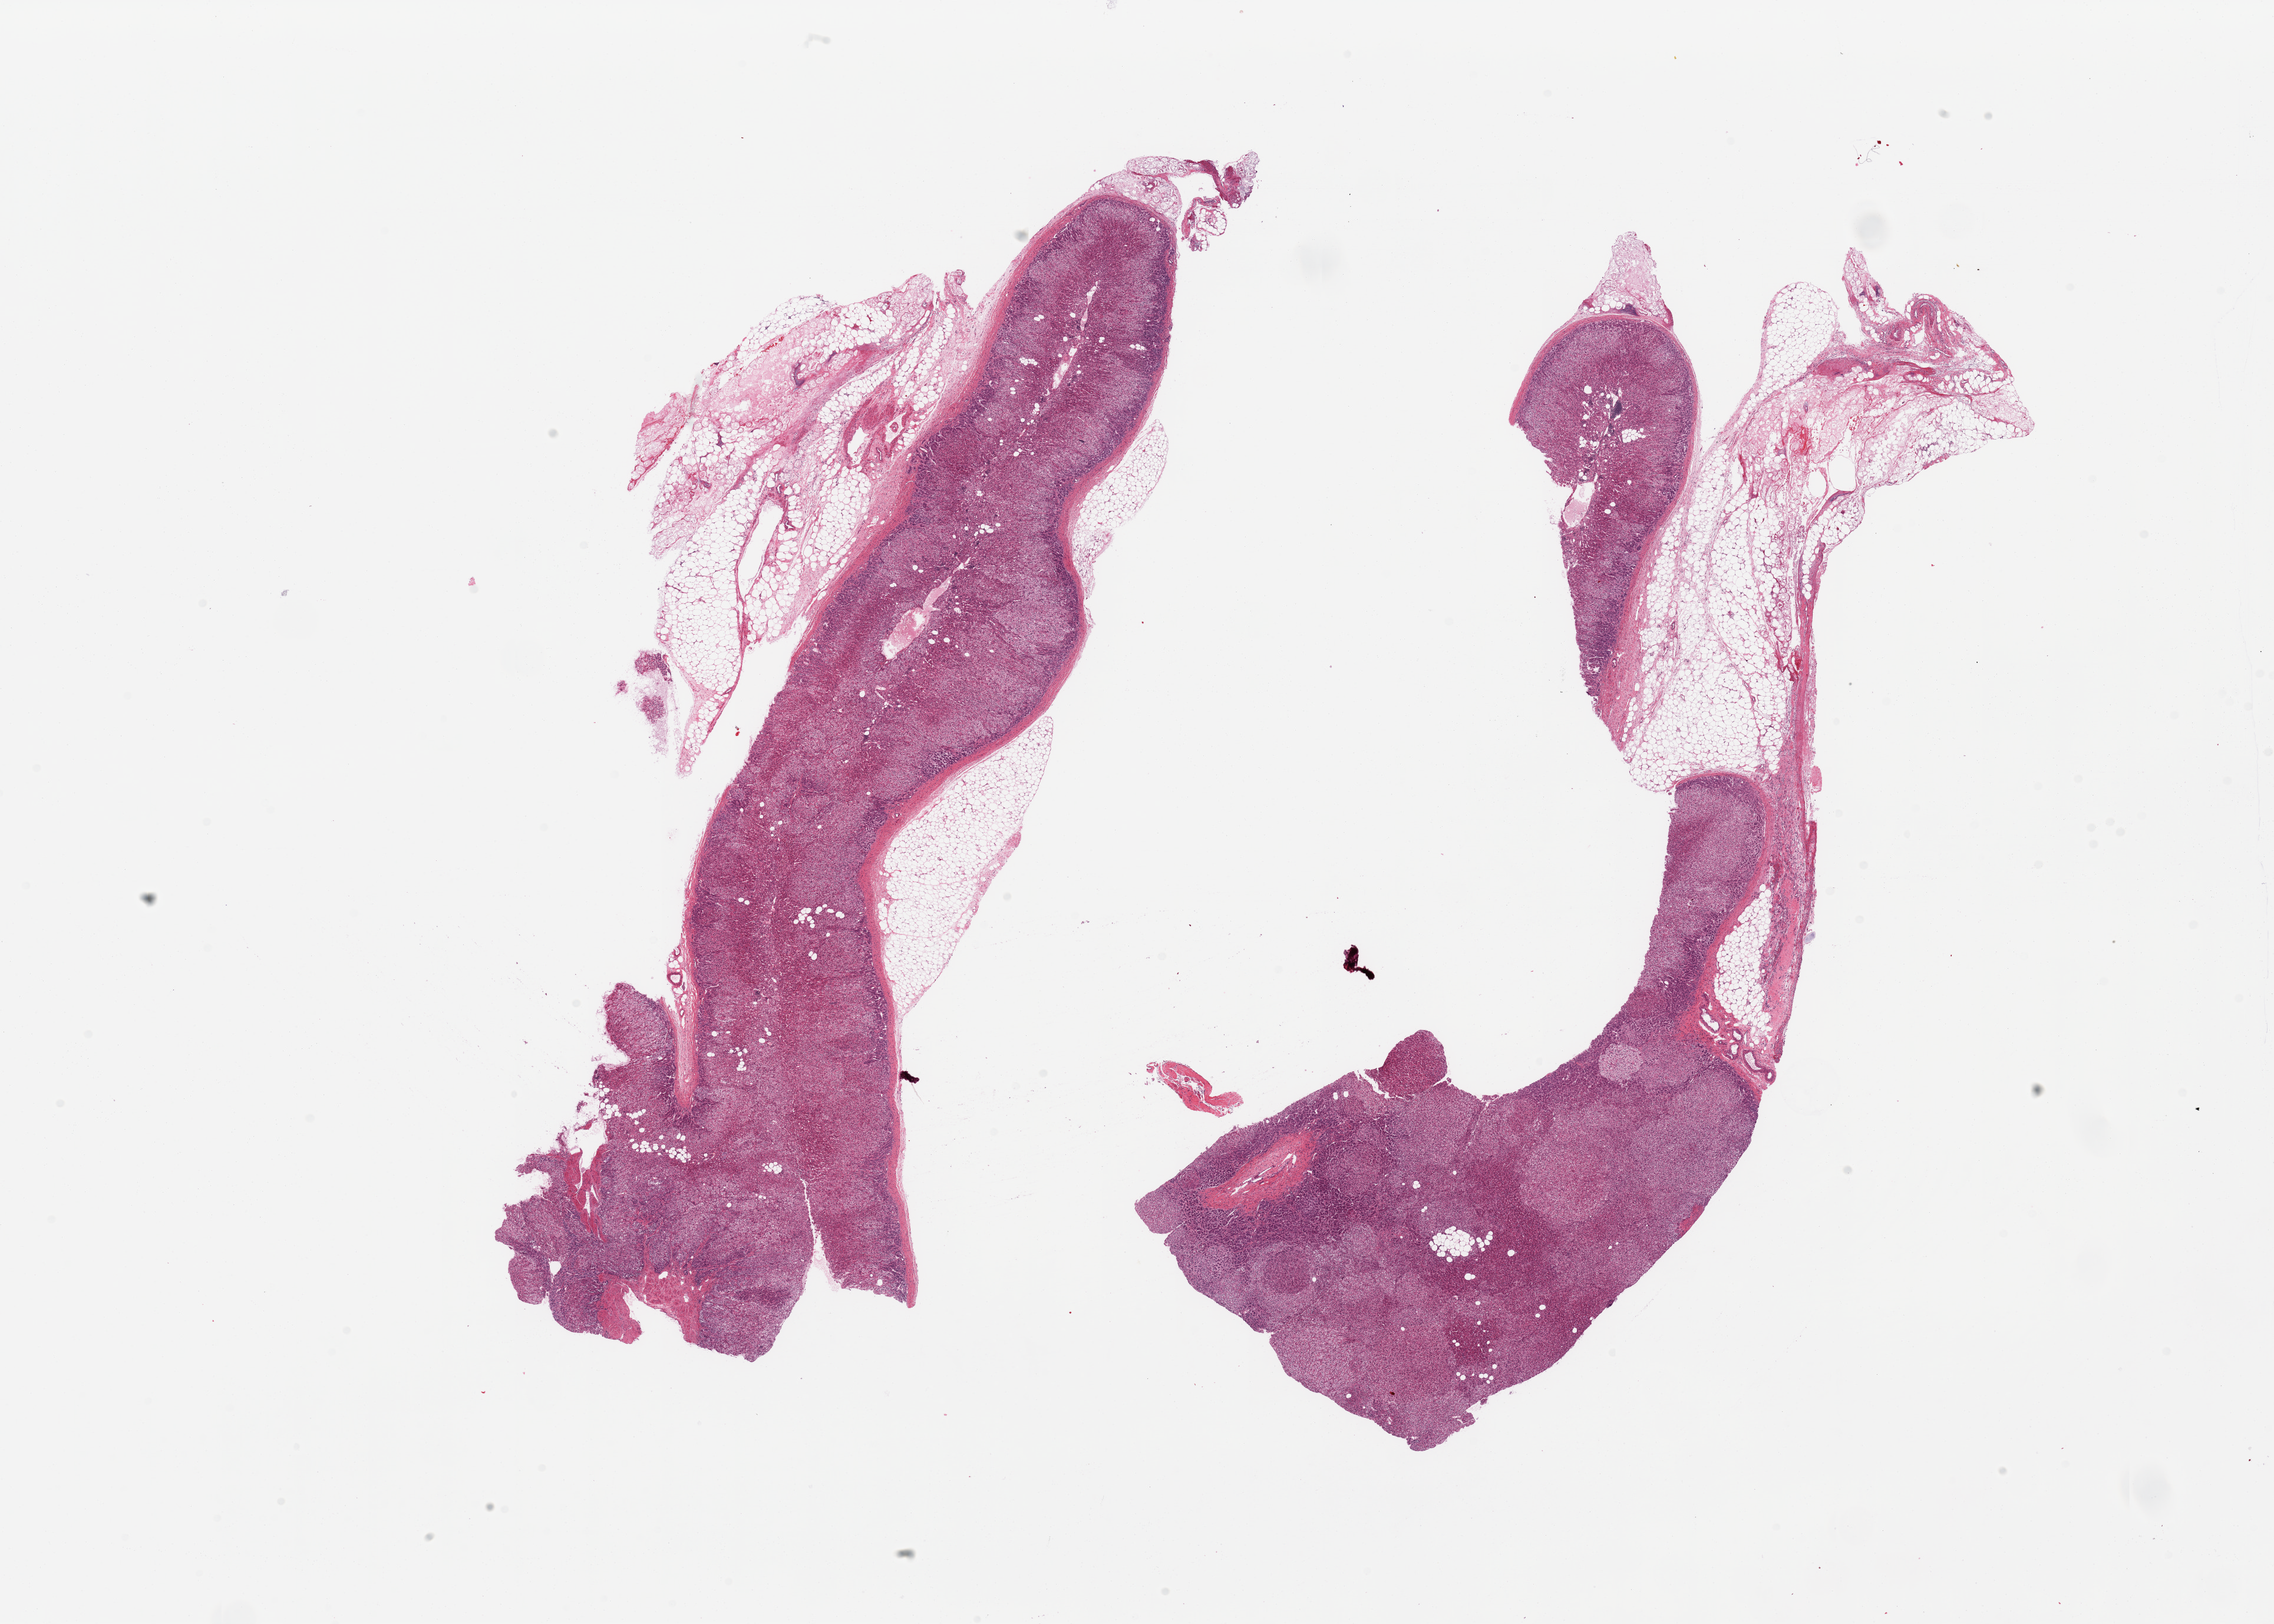
Hematoxylin and eosin (H&E) whole-slide image — a low-resolution overview of the entire scanned area, about 30.5 x 21.8 mm (acquisition: 20x scan); PAXgene-fixed paraffin-embedded (PFPE) section; target tissue: adrenal gland; tissue donor sample.
Pathologist's review note for this sample: 2 pieces, both with ~30% attached fat, fat necrosis.